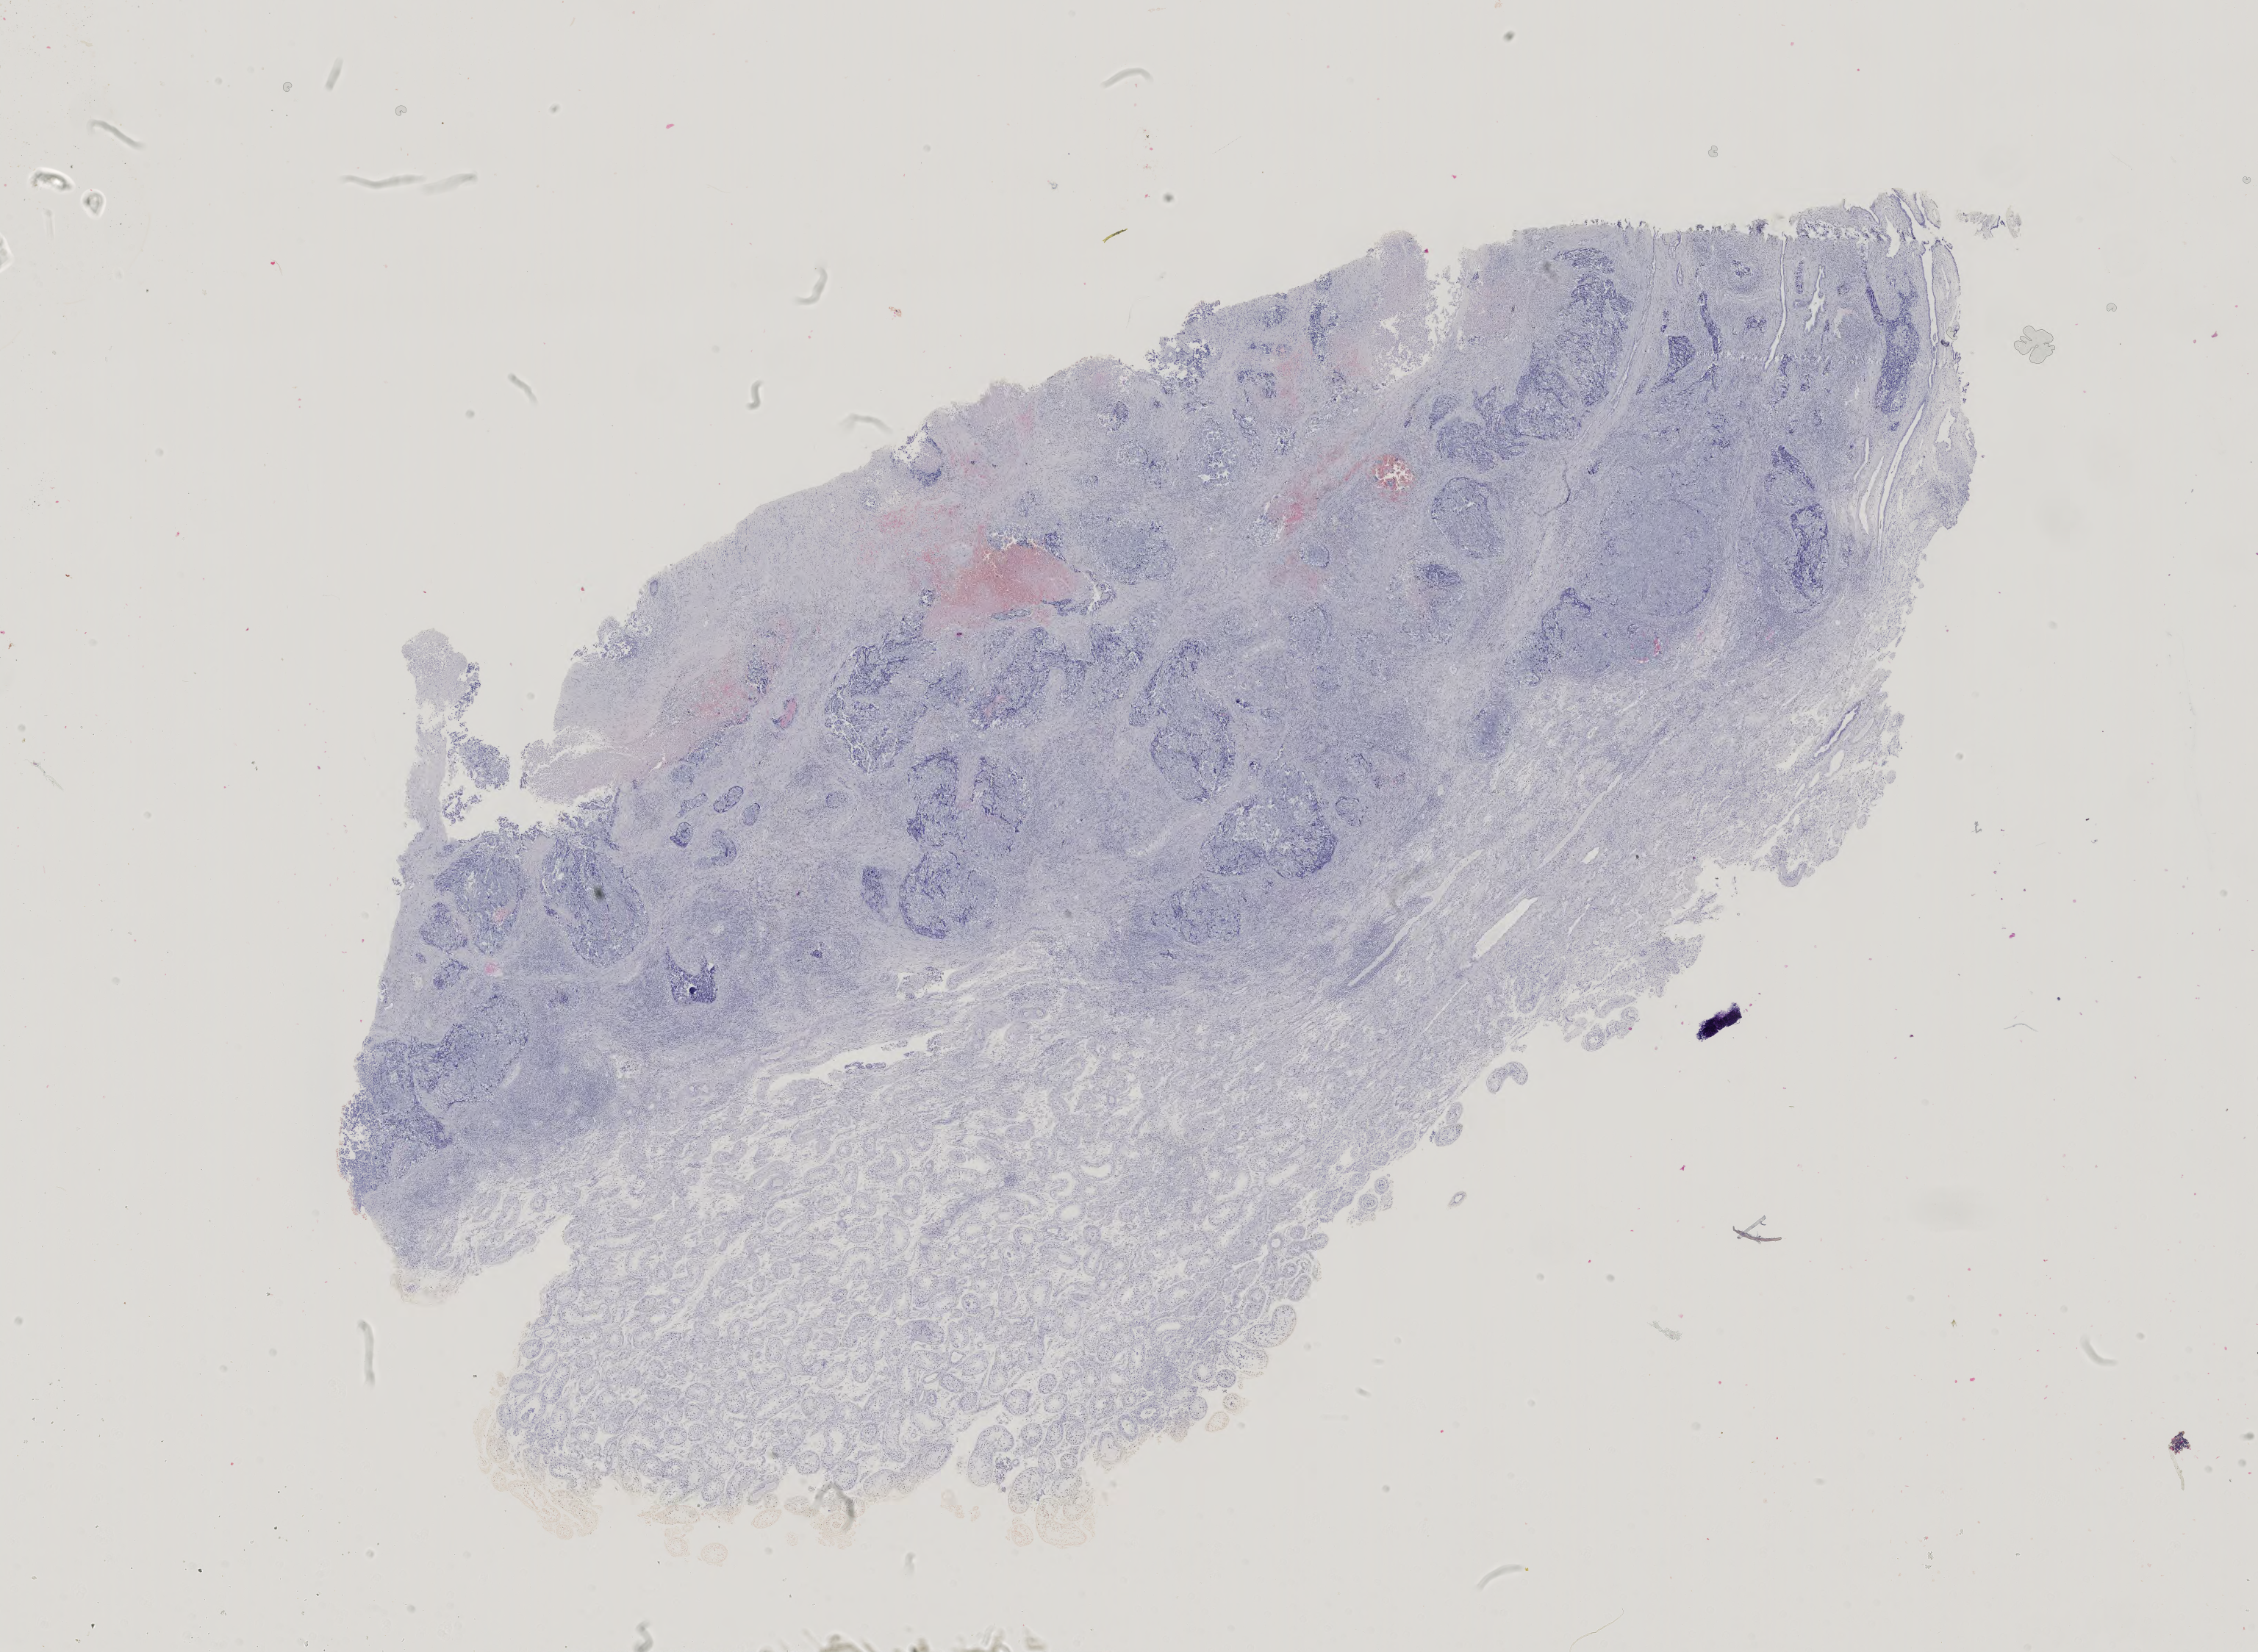
Whole-slide histology image, H&E-stained — whole scanned area (about 22.4 x 16.4 mm) shown as a low-resolution overview, formalin-fixed paraffin-embedded (FFPE) diagnostic section, primary tumour sample from the testis. Male patient; age at initial diagnosis 26 years.
Laterality: left. Pathologic diagnosis: Embryonal carcinoma, NOS. AJCC pathologic stage: II (4th edition). TNM: T2 NX M0.